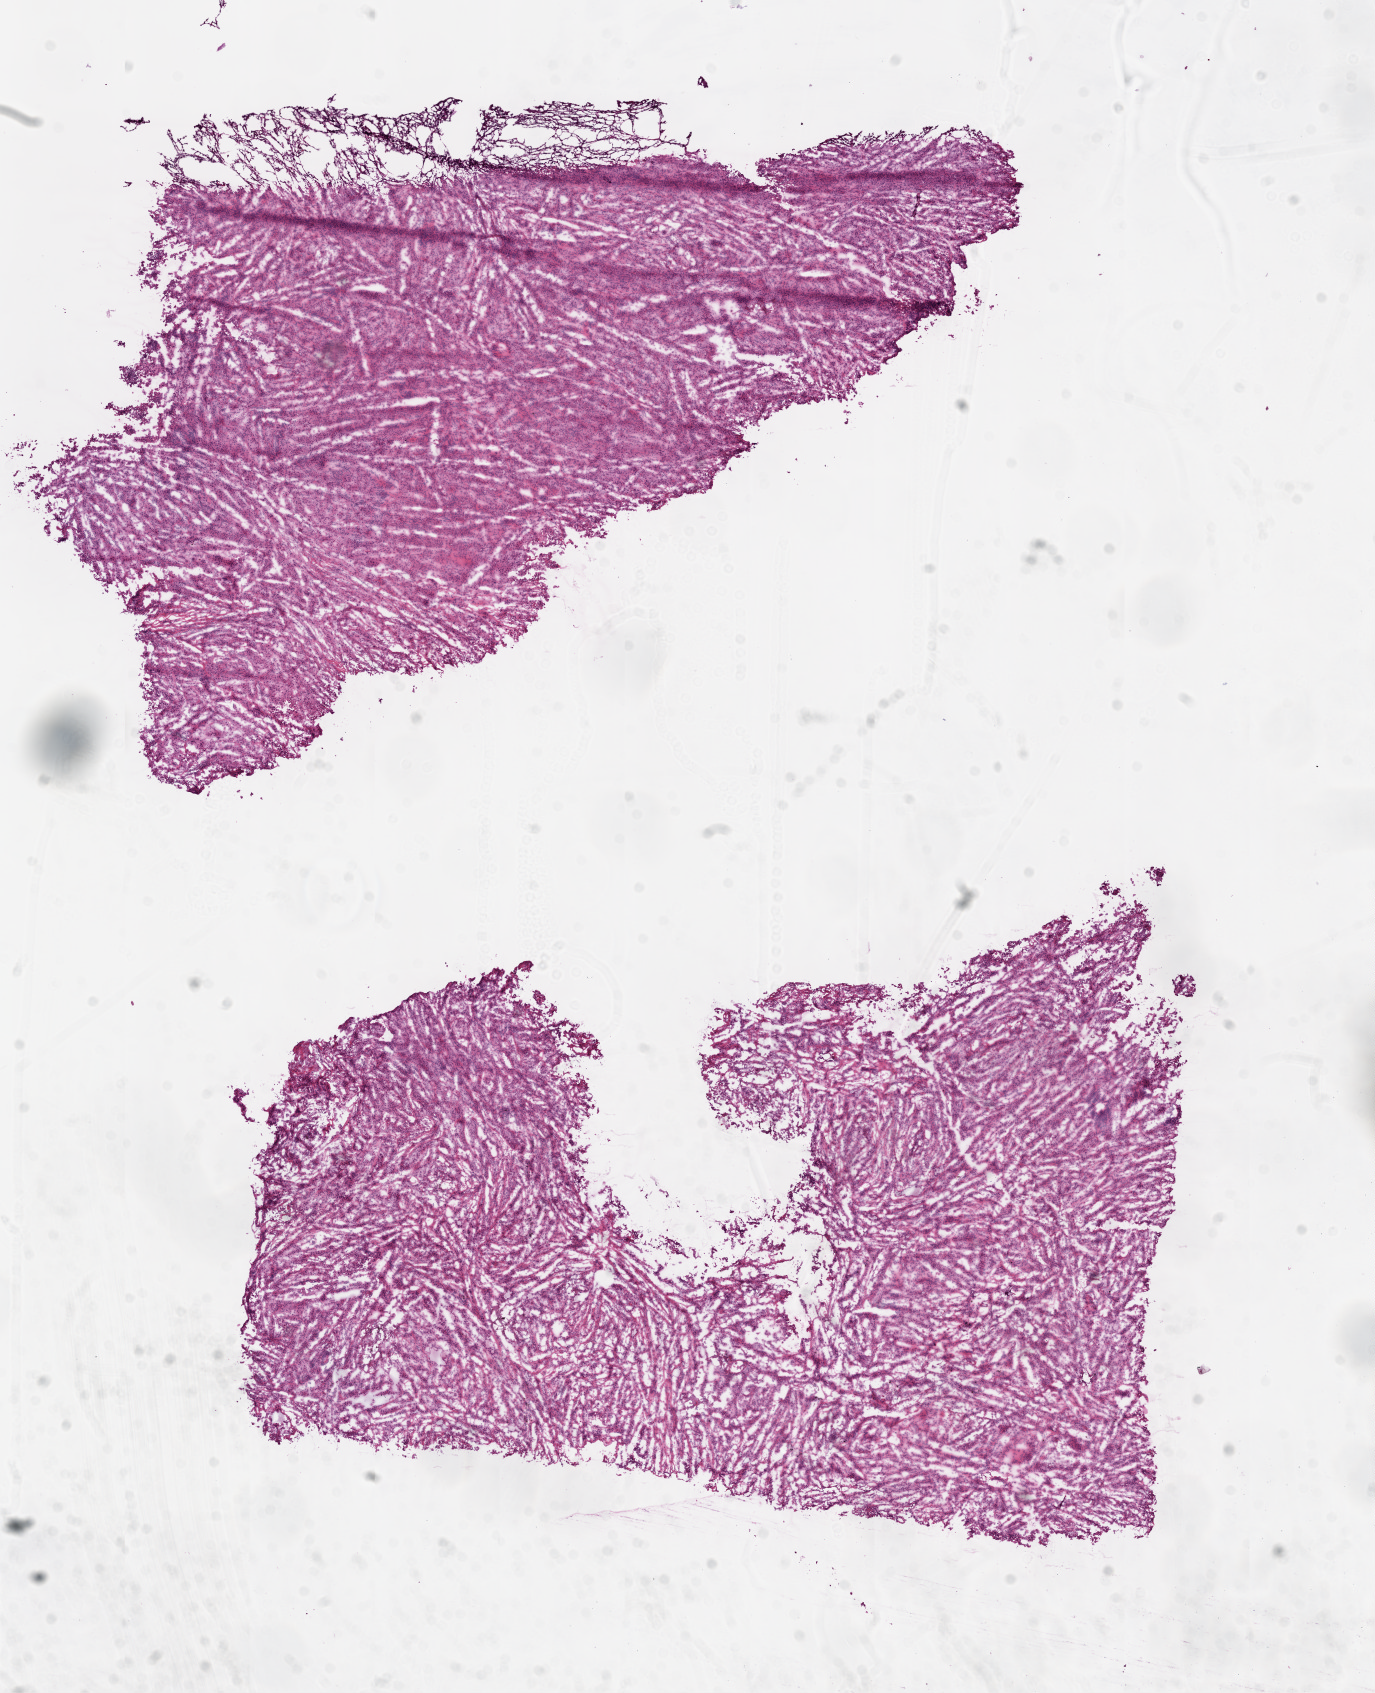
Whole-slide histology image, H&E-stained, low-resolution overview of the scanned area, about 11.0 x 13.6 mm (slide scanned at 20x). Frozen section from the top of the tissue portion. Primary tumour sample from the lung. Female, age 55 years at initial diagnosis. Pathologist review of this section (percent, as recorded): tumour cells 90%, tumour nuclei 75%.
Pathologic diagnosis: Adenocarcinoma with mixed subtypes (upper lobe, lung).